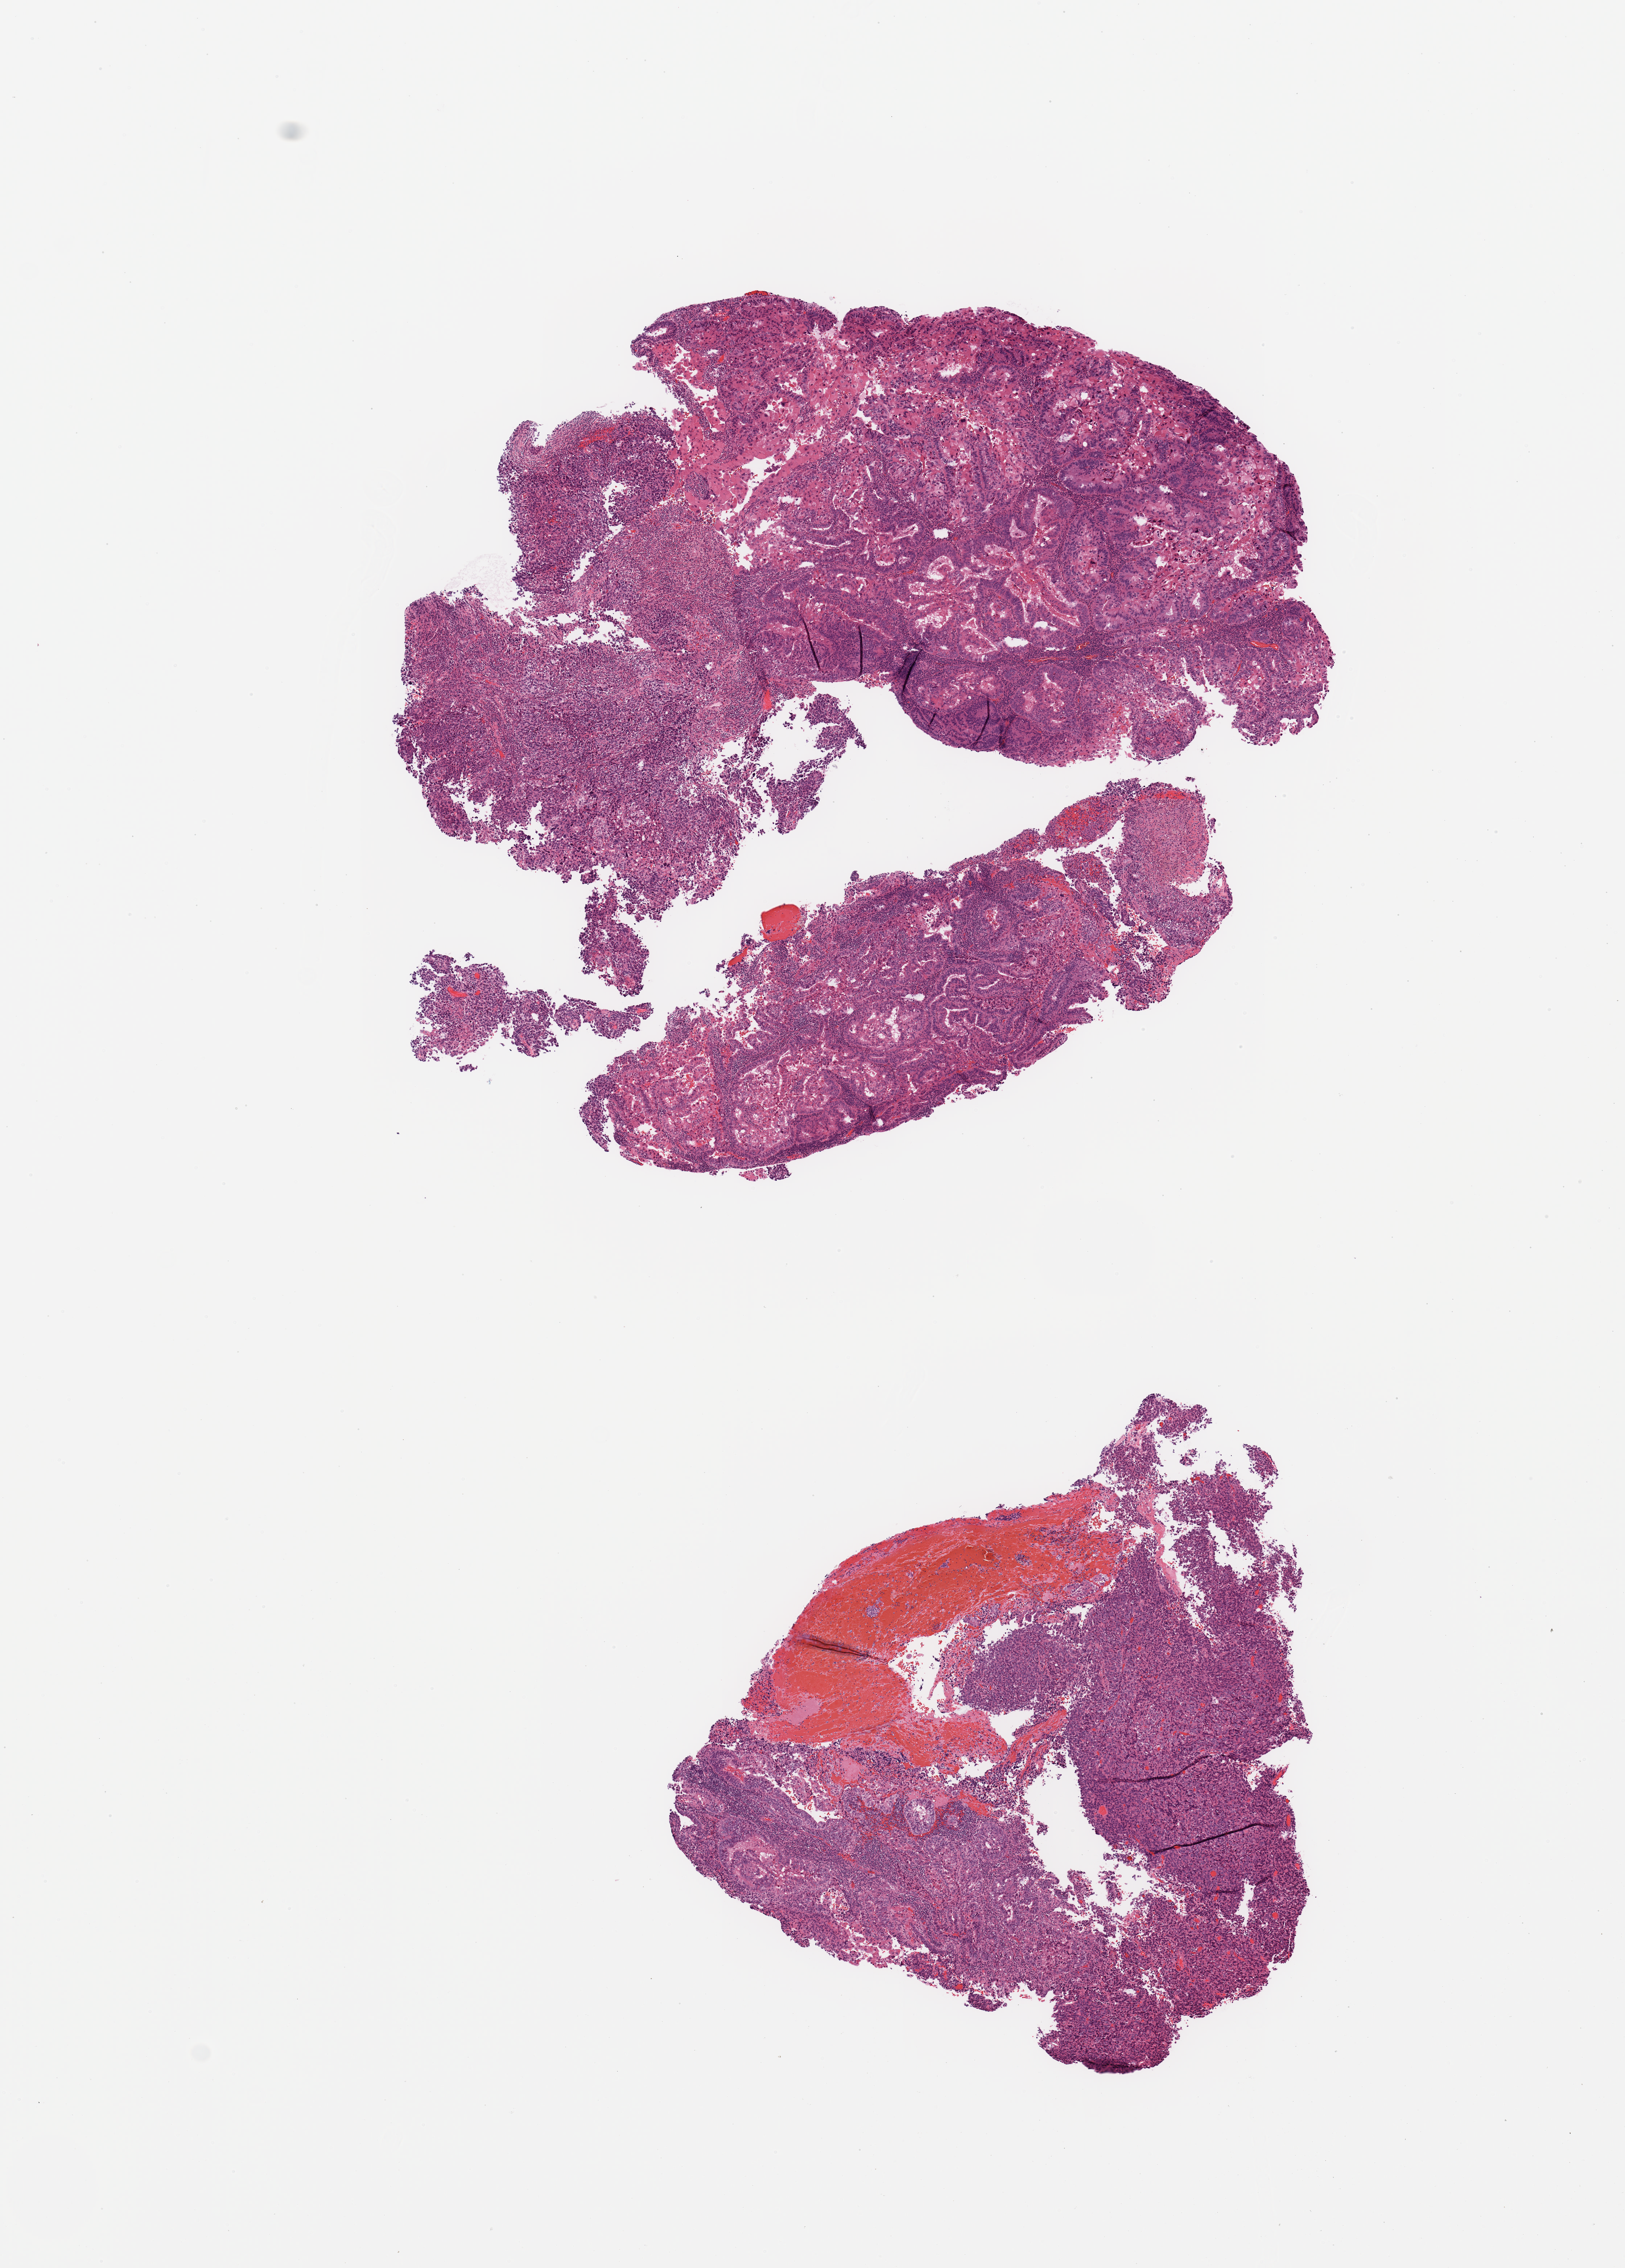
H&E whole-slide image, low-resolution overview of the scanned area, about 8.9 x 12.4 mm (from a 20x scan); uterus, tumour tissue. 60-year-old female patient. Histologic grade: G3 (poorly differentiated).
Diagnosis: Endometrioid adenocarcinoma, NOS. AJCC pathologic stage: I.